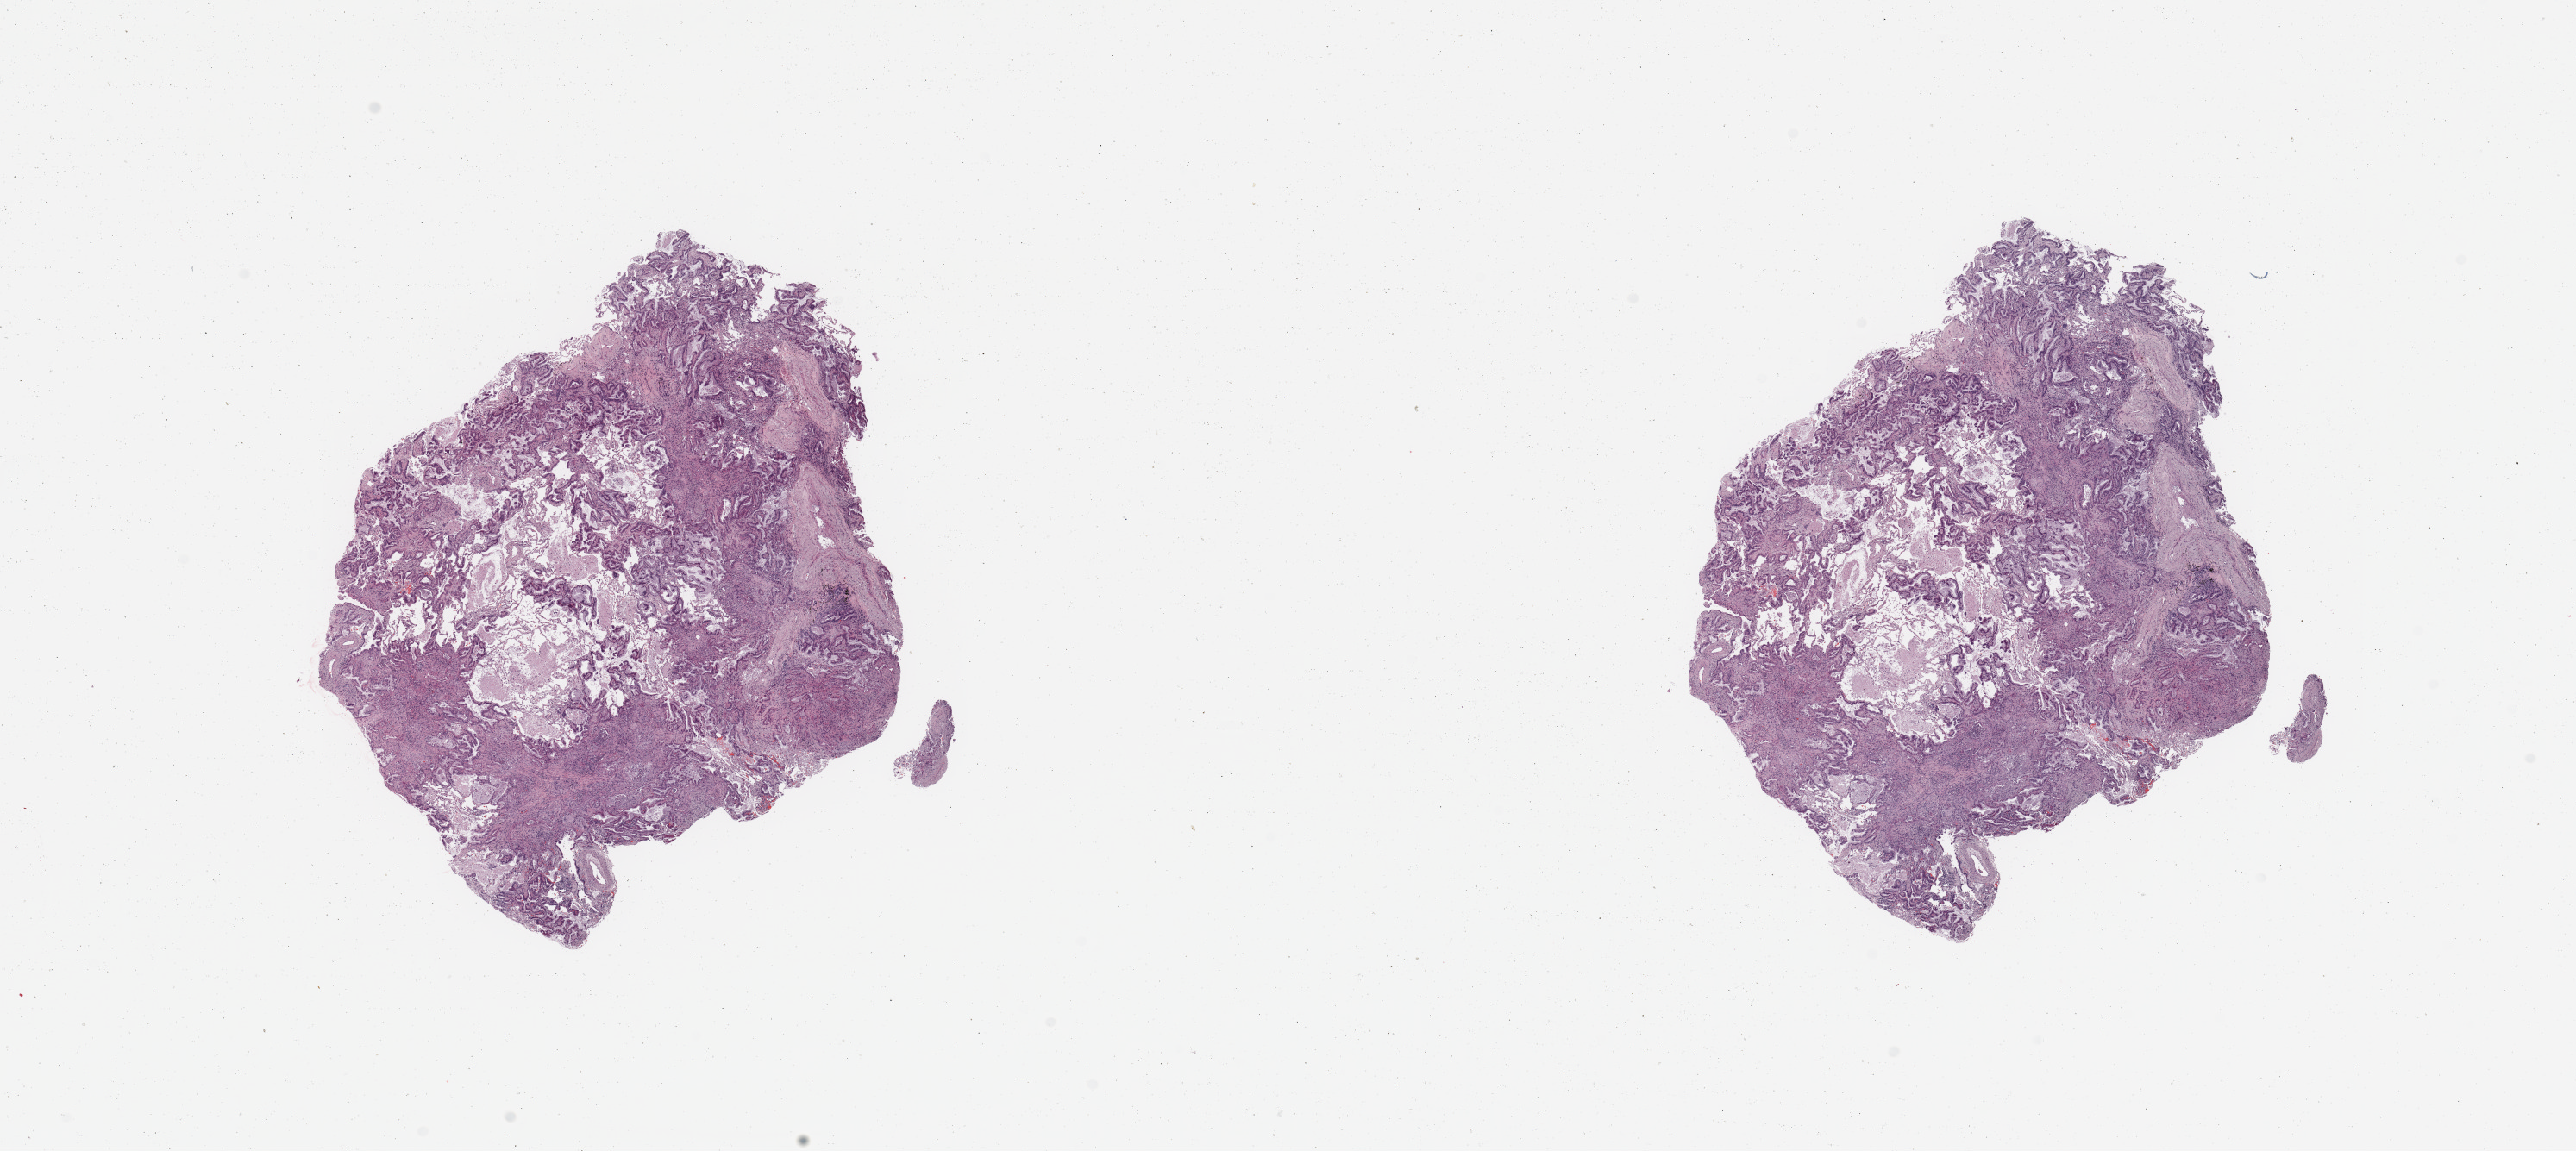
Digitized H&E tissue section (whole slide), low-resolution overview of the scanned area, about 23.6 x 10.6 mm. Tumour tissue sample, lung. Female, 79 y/o. Histologic grade: G1 (well differentiated).
Diagnosis: Adenocarcinoma, NOS. AJCC pathologic stage: IIB.